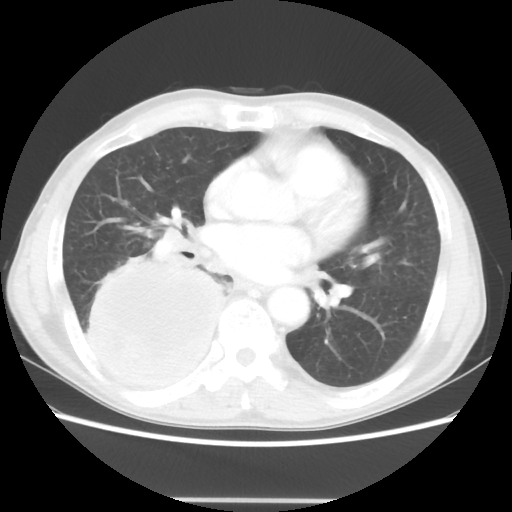
Chest CT, one axial slice; reconstruction kernel STANDARD; lung window (W 1500 / L -600 HU); 512 × 512 image matrix. Male patient, age 66 years. From the clinical record (not read from this slice): clinical TNM (as recorded): T4 N1 M1.
Annotated regions visible in this slice (rectangle marked by the reading radiologist):
- lung tumour (recorded histology: small cell carcinoma): box from (x=72, y=258) to (x=226, y=396) px